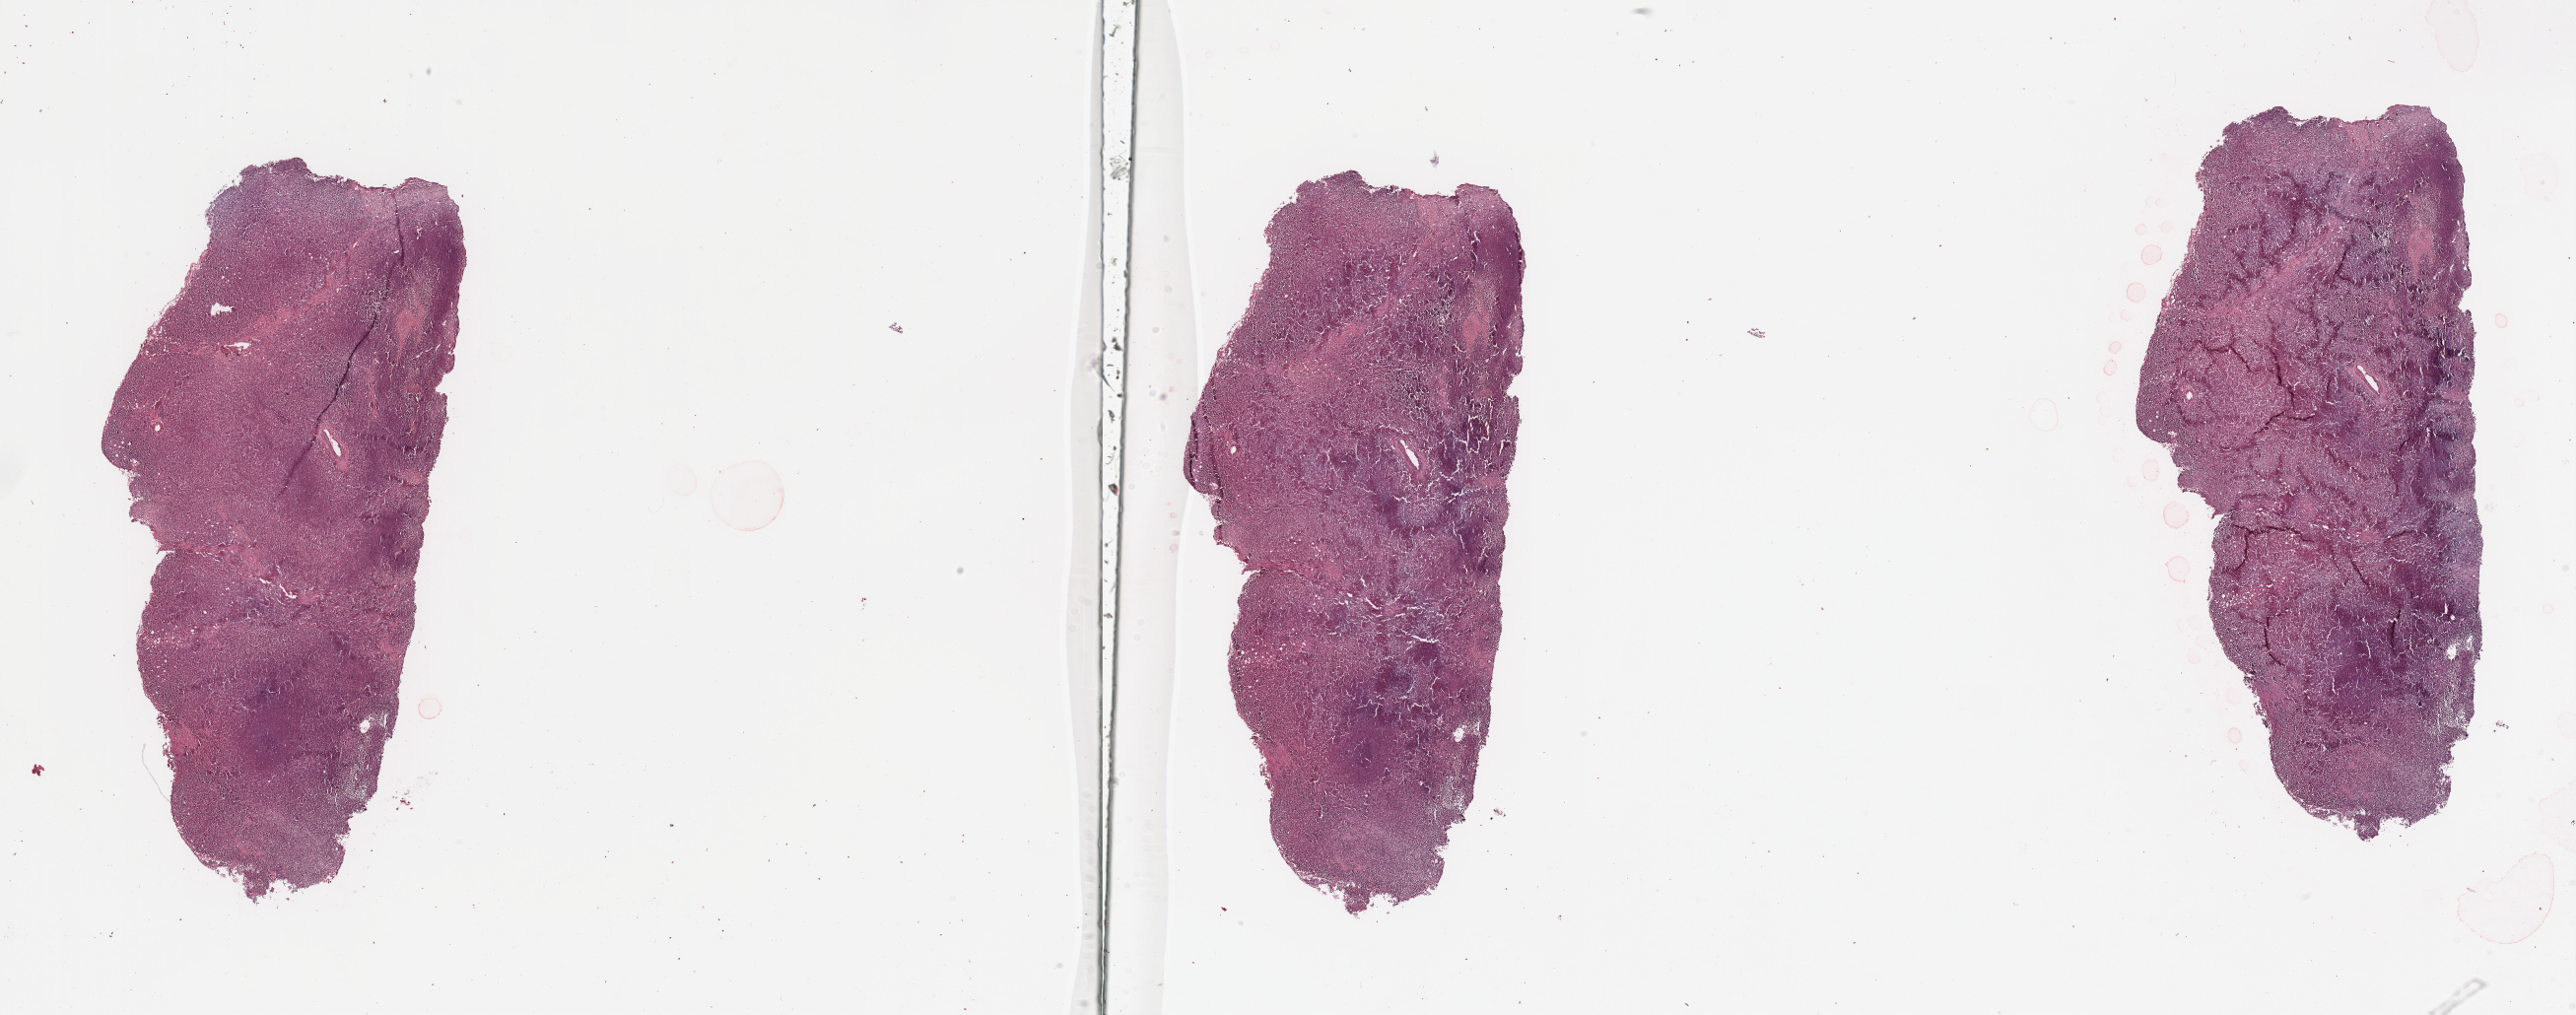
Digitized H&E-stained tissue section (whole slide) — low-resolution overview of the scanned area, about 41.3 x 16.3 mm (from a 20x scan). Tumour tissue sample, sampled site: trunk. Male, 45 y/o. Pathologist review of this section (percent, as recorded): tumour nuclei 95%, necrosis 1%.
This section: metastatic tumour tissue. Patient diagnosis: Malignant melanoma, NOS.